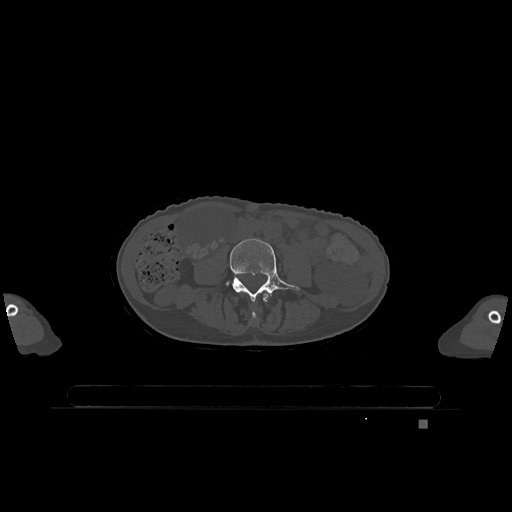
CT including the spine, one axial slice; position 302 of 1317 along the scan axis; bone window (W 1800 / L 400 HU); 0.5 mm slice thickness; 512 × 512 image matrix, field of view 500 × 500 mm. Patient: female, 74 years. From the clinical record (not read from this slice): primary cancer: lung; vertebrae with lytic lesions (as recorded): T1, T4, T5, T6, L4, L5.
Outlined on this slice (semi-automatically segmented with operator editing):
- L3 vertebra: box from (x=246, y=292) to (x=270, y=319) px
- L4 vertebra: (x=225, y=239)–(x=300, y=302)